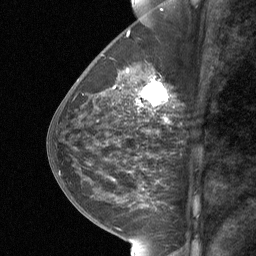
Breast MRI (dynamic contrast-enhanced), one sagittal slice. Position 28 of 64 along the scan axis. Dynamic contrast-enhanced study with each time point stored as its own series, time point 2 of 3 at this slice position (early post-contrast, ordered by acquisition time). 1.5 T. TE 4.8 ms, TR 27 ms. 256 × 256 image matrix. Patient: female, 59 years. Case-level facts recorded for this patient, not image findings: setting: breast cancer imaged before/during neoadjuvant chemotherapy; receptor status: triple-negative.
Annotated regions visible in this slice (semi-automatically segmented with operator editing):
- analysis volume of interest (the breast-tissue region the enhancement analysis was run in; not a lesion): box from (x=127, y=66) to (x=171, y=122) px
- tumour enhancement mask (voxels above the 90 % enhancement threshold inside the analysis volume of interest): (x=137, y=79)–(x=168, y=105)